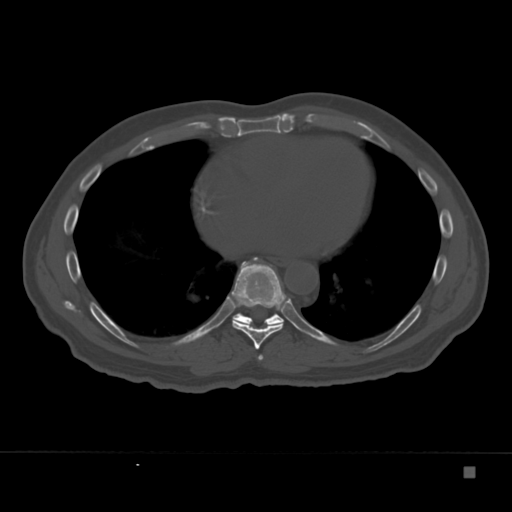
CT including the spine, one axial slice. Position 201 of 332 along the scan axis. Reconstruction kernel Br40s. Bone window (W 1800 / L 400 HU). 1.5 mm slice thickness. 512 × 512 image matrix, field of view 389 × 389 mm. Male patient, age 72 years. Case-level facts recorded for this patient, not image findings: primary cancer: skeletal.
Outlined on this slice (semi-automatic segmentation, software-assisted and operator-edited):
- T7 vertebra: box from (x=258, y=355) to (x=263, y=360) px
- T8 vertebra: (x=231, y=257)–(x=288, y=350)
- T9 vertebra: (x=232, y=257)–(x=284, y=327)